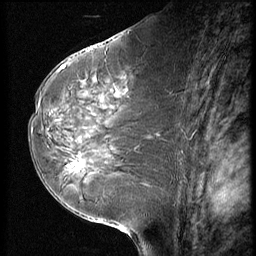
Breast MRI (dynamic contrast-enhanced), one sagittal slice. Slice 30 of 56 in the series (ordered by position). Dynamic contrast-enhanced series, image 2 of 3 at this slice position (ordered by acquisition). 1.5 T. TE 4.2 ms, TR 9 ms. 2.5 mm slice thickness. 256 × 256 image matrix, field of view 180 × 180 mm. Patient: female, 58 years. From the clinical record (not read from this slice): setting: breast cancer imaged before/during neoadjuvant chemotherapy; receptor status: HR-positive, HER2-negative.
Structures marked on this image (semi-automatic segmentation, software-assisted and operator-edited):
- analysis volume of interest (the breast-tissue region the enhancement analysis was run in; not a lesion): box from (x=56, y=146) to (x=99, y=182) px
- tumour enhancement mask (voxels above the 140 % enhancement threshold inside the analysis volume of interest): (x=66, y=160)–(x=85, y=171)